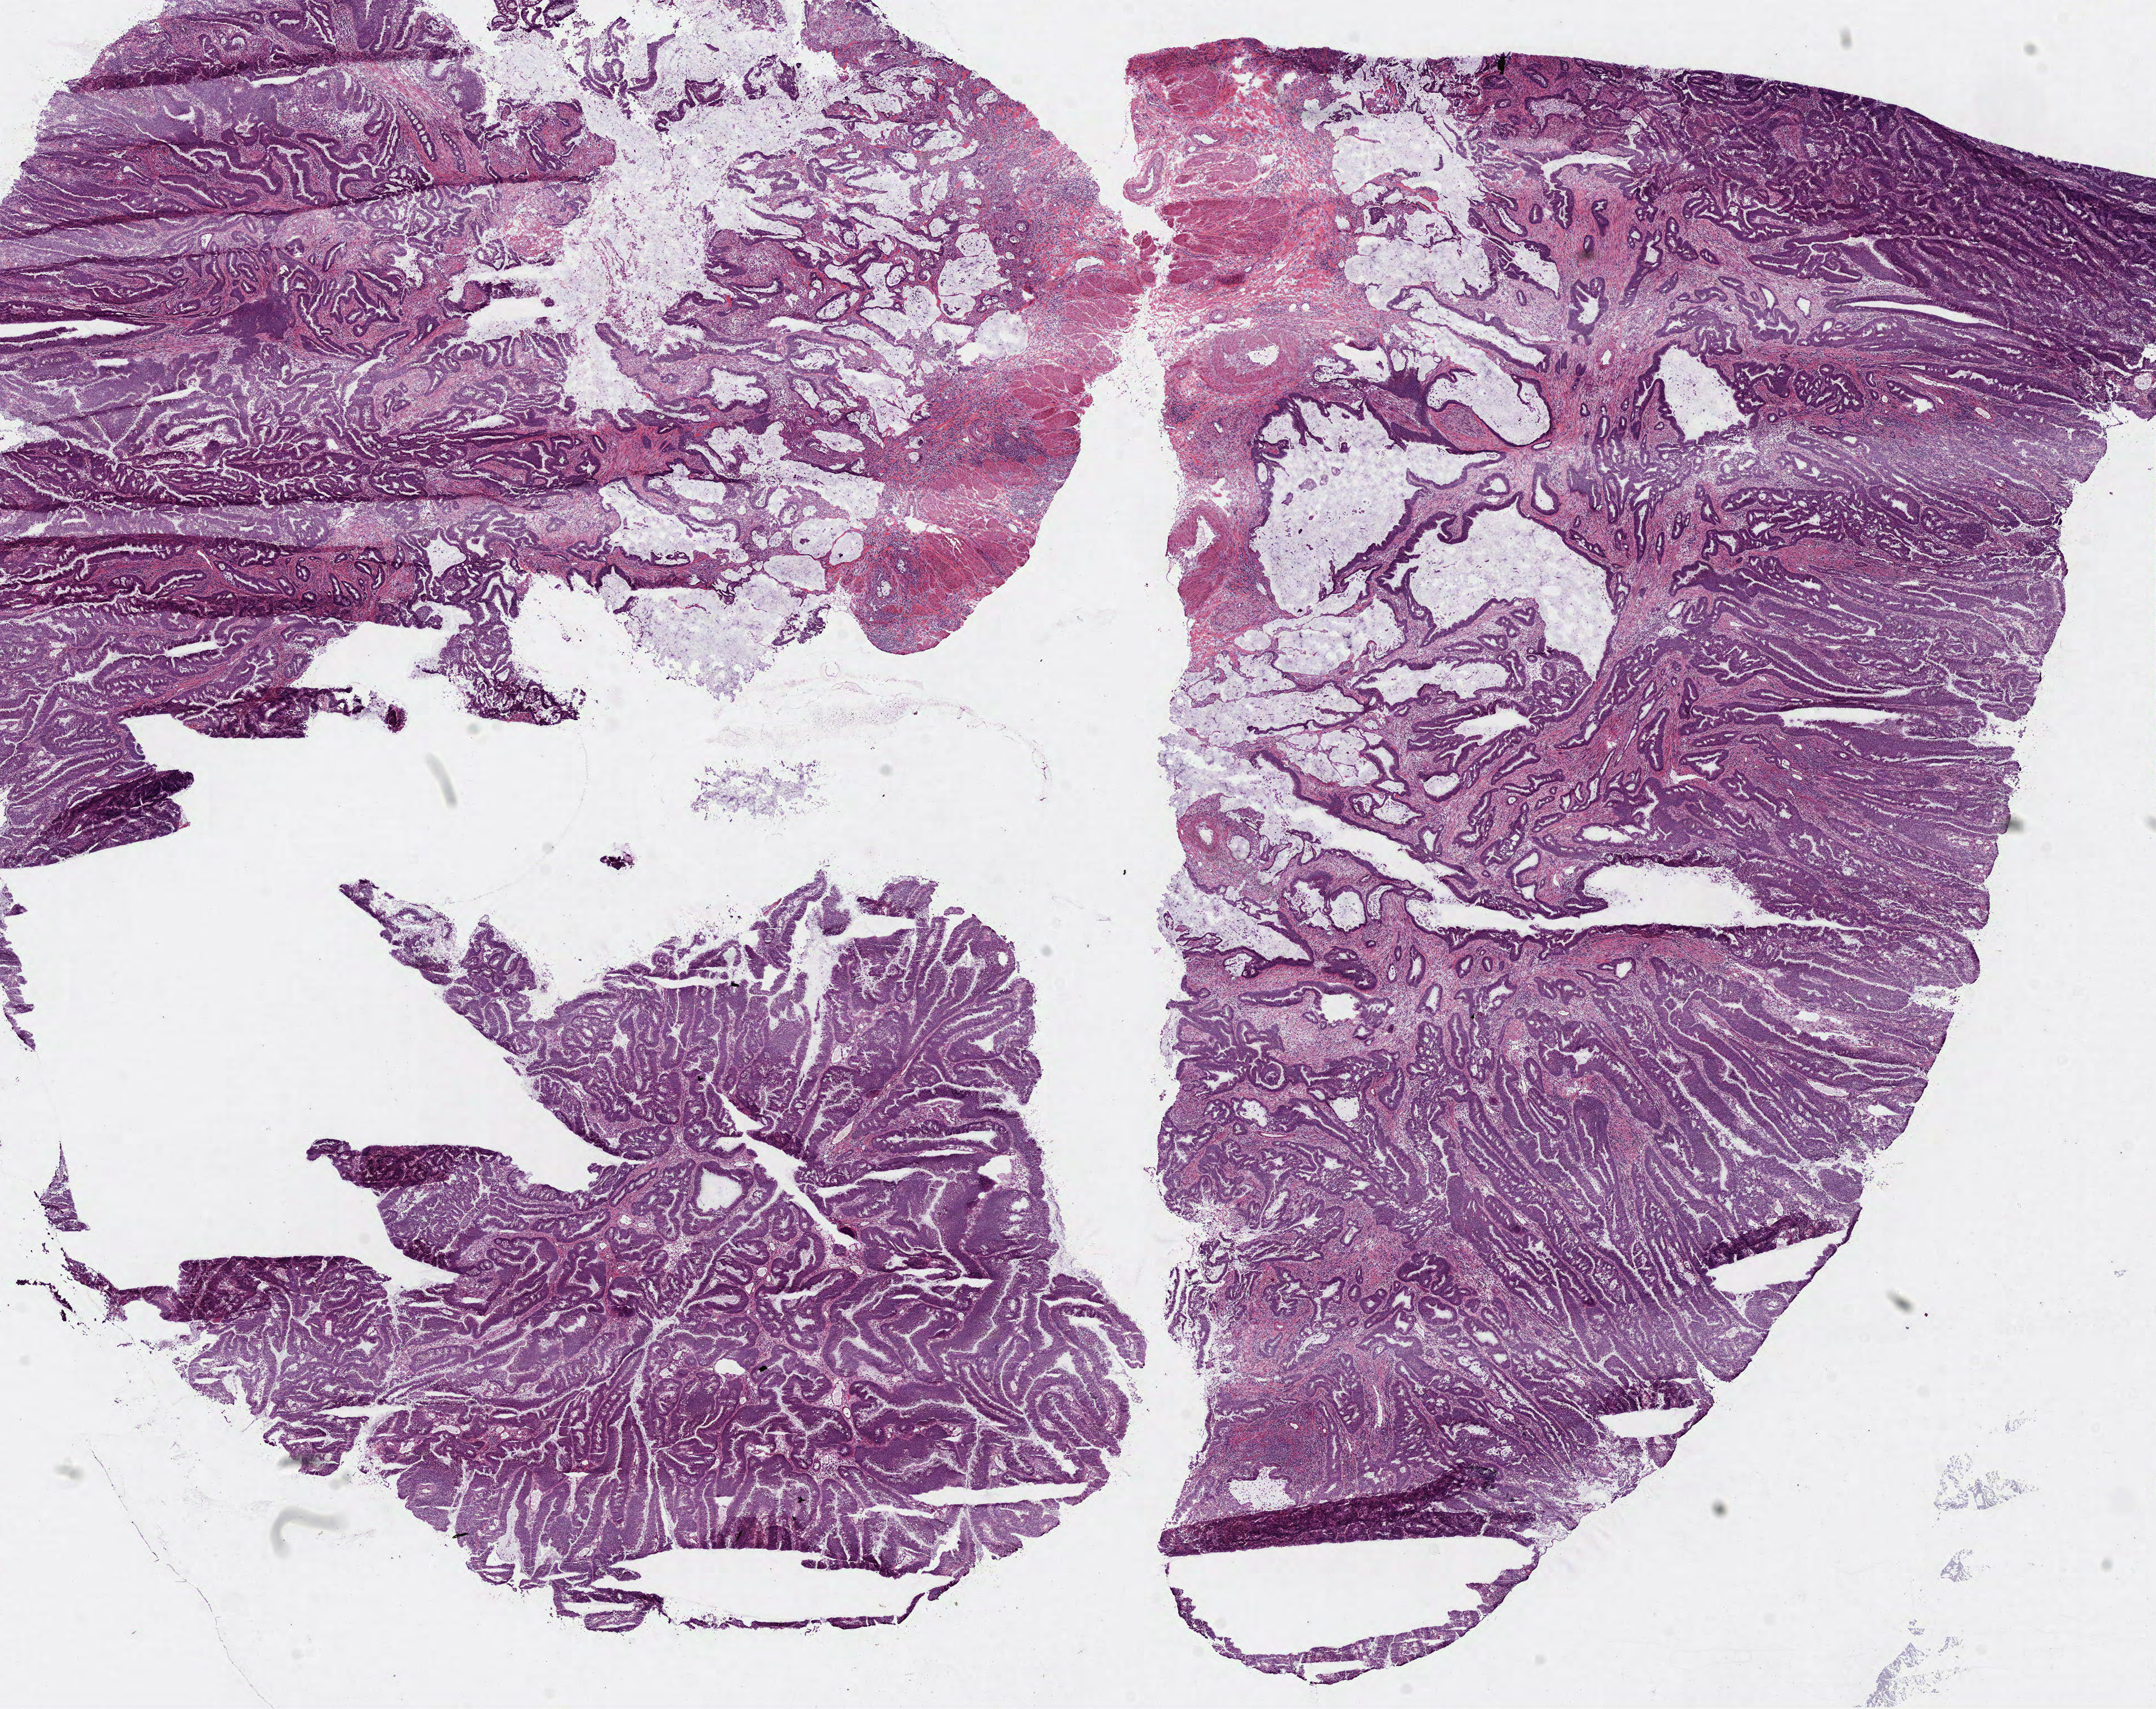
Whole-slide histology image, H&E — a low-resolution overview of the entire scanned area, about 15.6 x 12.3 mm (slide scanned at 40x), frozen section from the bottom of the tissue portion, primary tumour sample from the colon. Female, age 78 years at initial diagnosis. Pathologist review of this section (percent, as recorded): tumour cells 83%, tumour nuclei 80%, normal cells 5%, stromal cells 12%, necrosis 0%.
Pathologic diagnosis: Adenocarcinoma, NOS (cecum). AJCC pathologic stage: IIIB (7th edition).